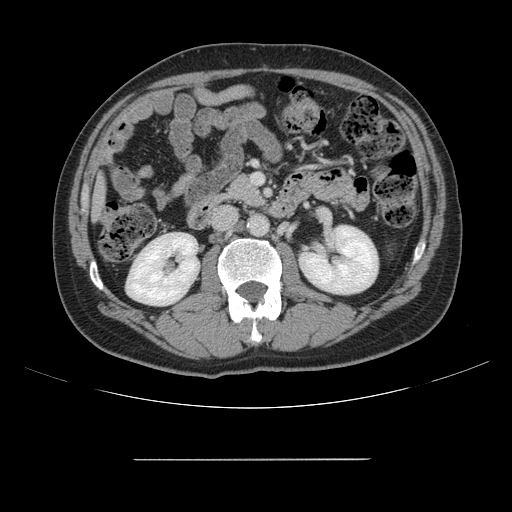
Contrast-enhanced abdominal CT, one axial slice. Slice 52 of 164 in the series (ordered by position). Intravenous contrast given. Soft-tissue window (W 400 / L 40 HU). 512 × 512 image matrix, field of view 404 × 404 mm. Male patient, age 54 years. Case-level facts recorded for this patient, not image findings: diagnosis: colorectal cancer liver metastases, imaged before liver resection; multiple liver metastases: yes; largest metastasis: 1 cm; disease in both lobes: no.
Outlined on this slice (outlined manually by an expert reader):
- liver: bounding box (x1, y1, x2, y2) in pixels: (95, 182, 104, 215)
- planned liver remnant (the part of the liver to remain after resection): (94, 183, 104, 216)